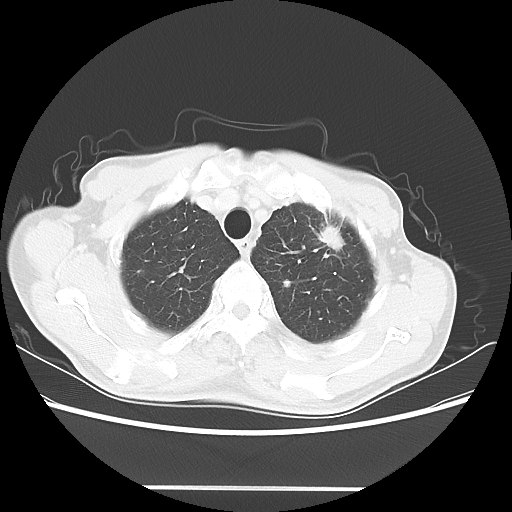
Chest CT, one axial slice; slice 50 of 60 in the series (ordered by position); lung window (W 1500 / L -600 HU); 5 mm slice thickness; 512 × 512 image matrix, field of view 367 × 367 mm. Male patient, age 74 years. From the clinical record (not read from this slice): clinical TNM (as recorded): T1c N0 M1a.
Annotated regions visible in this slice (rectangle marked by the reading radiologist):
- lung tumour (recorded histology: adenocarcinoma): bounding box [x1, y1, x2, y2] px = [317, 222, 346, 252]